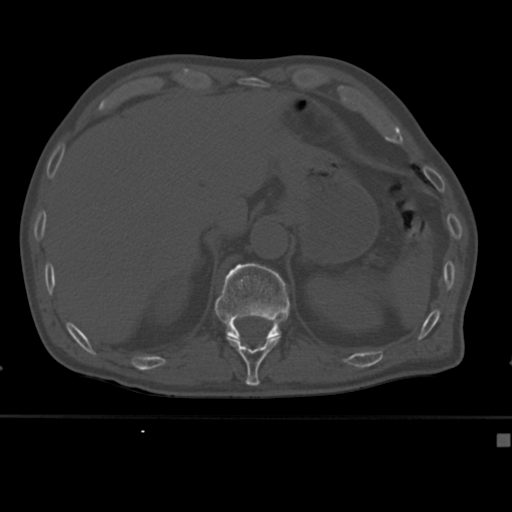
CT including the spine, one axial slice. Slice 200 of 430 in the series (ordered by position). 120 kVp. Bone window (W 1800 / L 400 HU). 1.5 mm slice thickness. 512 × 512 image matrix, field of view 337 × 337 mm. Patient: male, 64 years. Case-level facts recorded for this patient, not image findings: primary cancer: uterus; vertebrae with lytic lesions (as recorded): T1, T4, T5, T7, L5.
Structures marked on this image (semi-automatically segmented with operator editing):
- T11 vertebra: bounding box (x1, y1, x2, y2) in pixels: (226, 336, 280, 382)
- T12 vertebra: (214, 263, 290, 340)